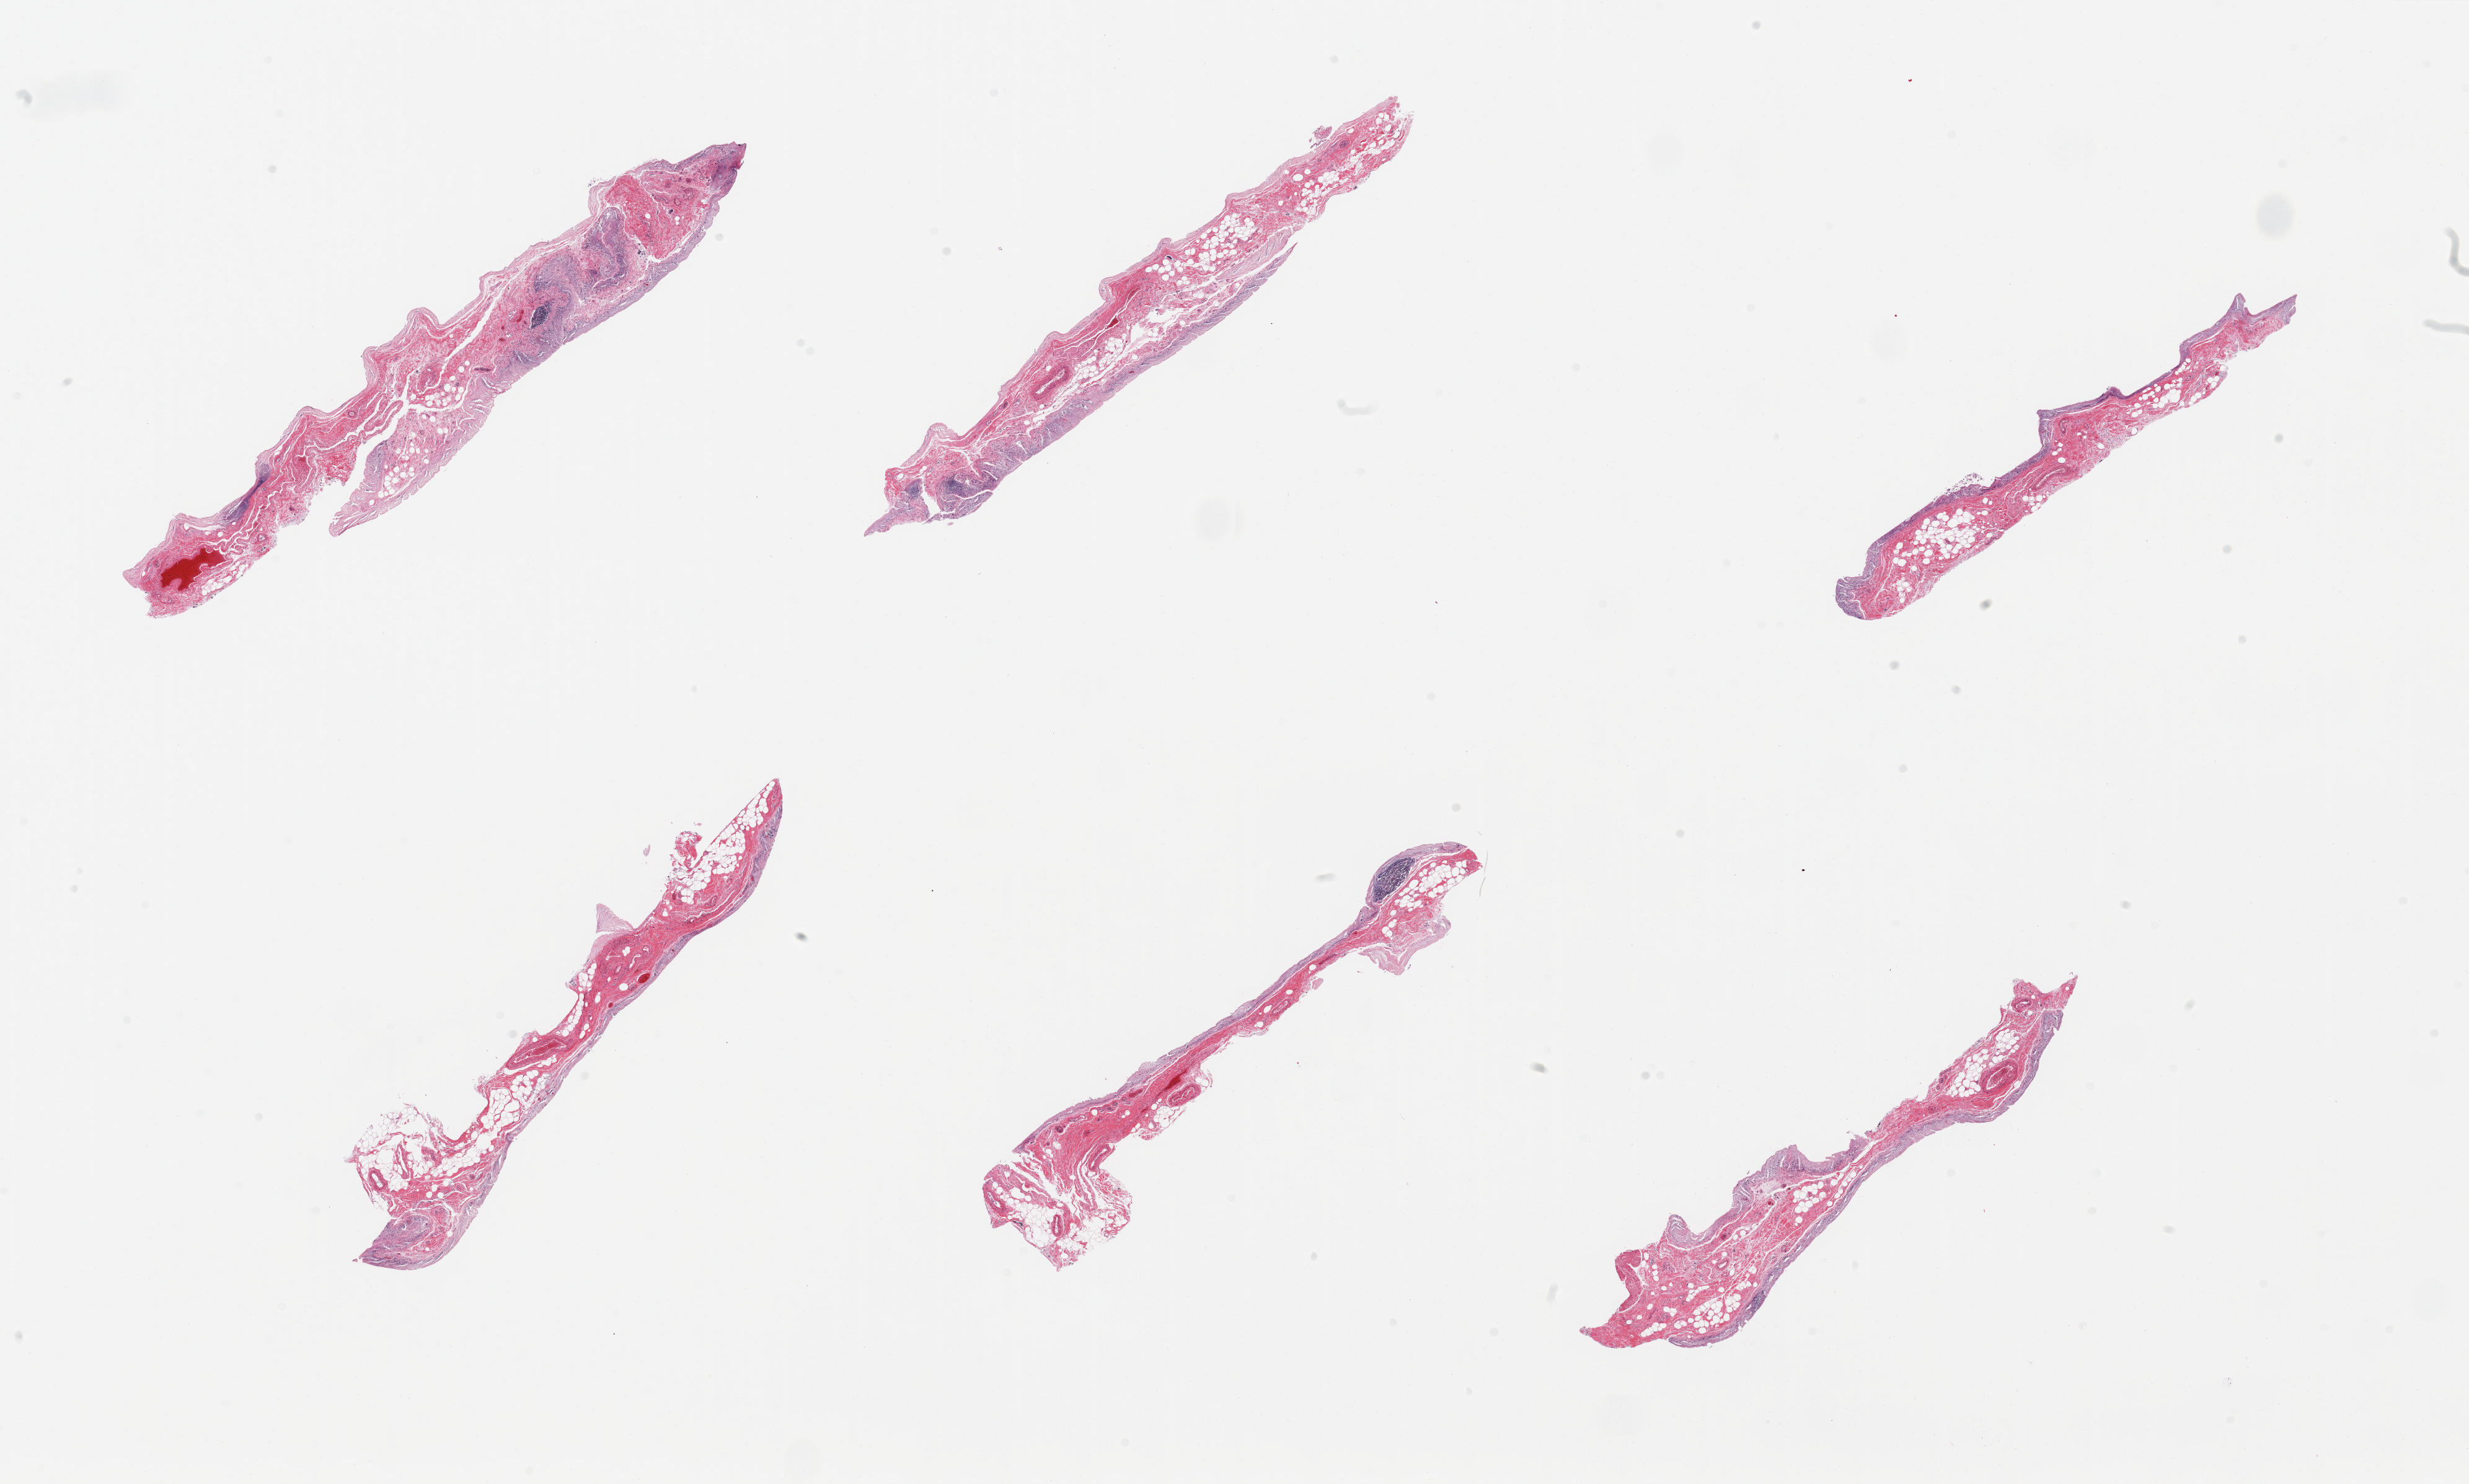
Hematoxylin and eosin (H&E) whole-slide image, whole scanned area (about 31.5 x 18.9 mm, from a 20x scan) shown as a low-resolution overview. PAXgene-fixed, paraffin-embedded tissue. Section of transverse colon (target tissue). Donor tissue sample.
Reviewer comment on this tissue sample: 6 pieces; totally autolyzed mucosa; no muscularis propria.